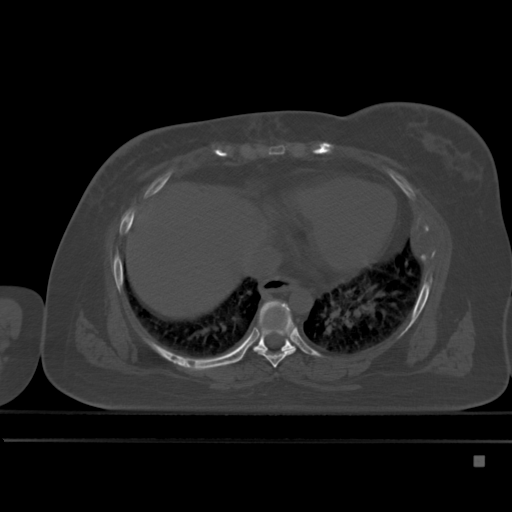
CT including the spine, one axial slice; slice 285 of 495 in the series (ordered by position); bone window (W 1800 / L 400 HU); 1.5 mm slice thickness; 512 × 512 image matrix, field of view 404 × 404 mm. Female patient, age 33 years. From the clinical record (not read from this slice): primary cancer: breast.
Structures marked on this image (semi-automatically segmented with operator editing):
- T7 vertebra: bounding box <259,315,297,368> (left, top, right, bottom; pixels)
- T8 vertebra: <242,298,295,358>